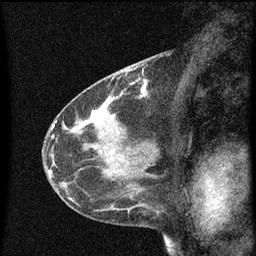
Breast MRI (dynamic contrast-enhanced), one sagittal slice; slice 29 of 60 in the series (ordered by position); dynamic contrast-enhanced series, image 2 of 3 at this slice position (ordered by acquisition); 1.5 T; TE 4.2 ms, TR 8 ms; 2 mm slice thickness; 256 × 256 image matrix. Patient: female, 41 years.
Structures marked on this image (semi-automatic segmentation, software-assisted and operator-edited):
- analysis volume of interest (the breast-tissue region the enhancement analysis was run in; not a lesion): bounding box (x1, y1, x2, y2) in pixels: (130, 76, 155, 99)
- tumour enhancement mask (voxels above the 70 % enhancement threshold inside the analysis volume of interest): (140, 80, 149, 99)